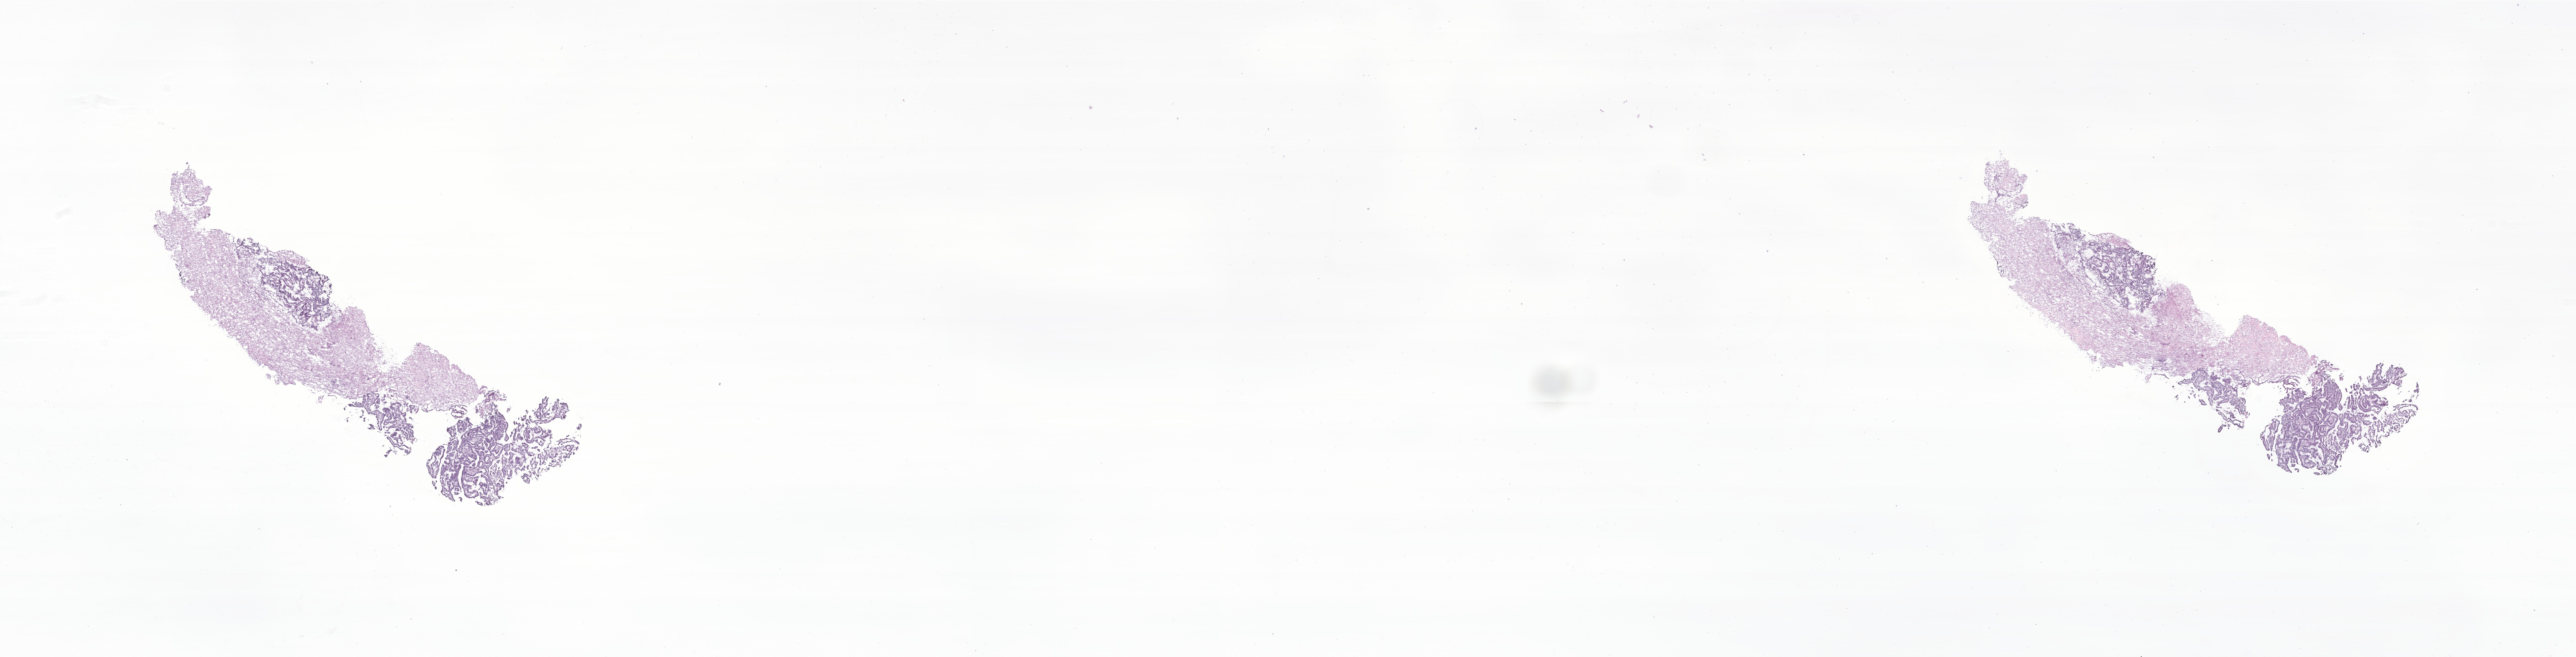
Digitized haematoxylin and eosin-stained section of tumor tissue from the brain, shown as a low-resolution overview of the whole scanned area (about 32.2 x 8.2 mm). Frozen section. Male patient, age 115 months (9 years 7 months).
Diagnosis: Atypical choroid plexus papilloma.